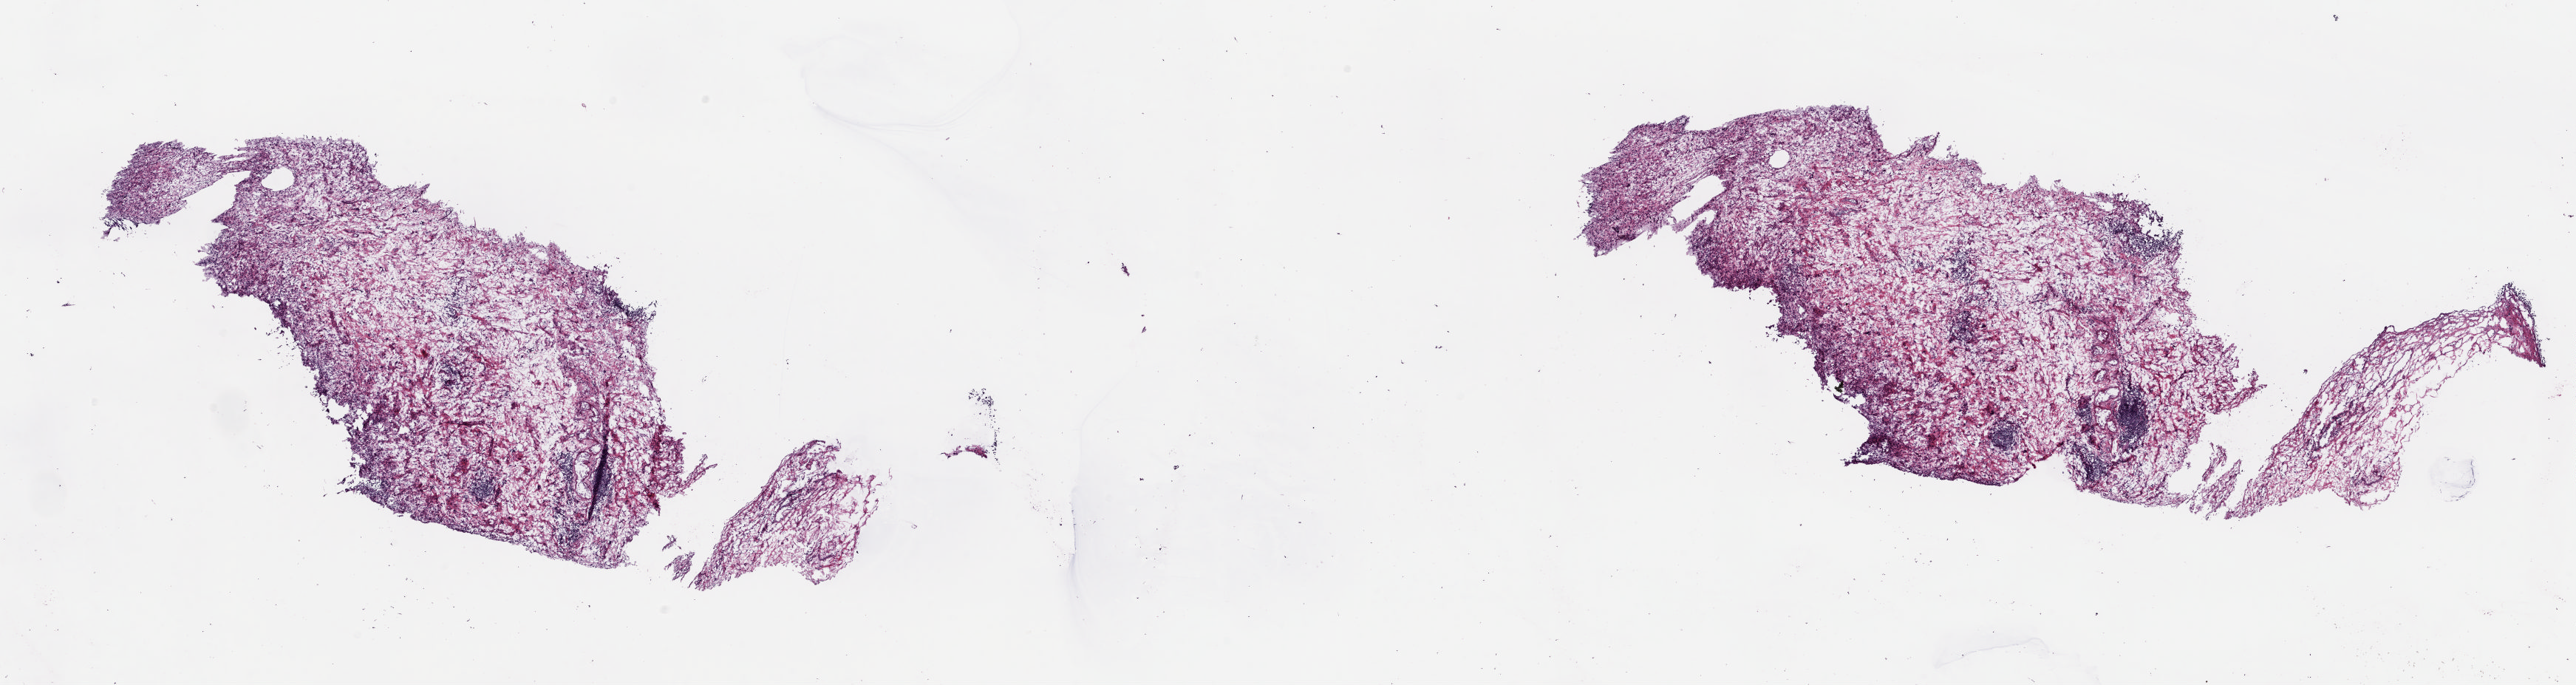
Hematoxylin and eosin (H&E) stained whole-slide image — low-resolution overview of the scanned area, about 27.7 x 7.4 mm (acquisition: 20x scan); frozen section; bladder, solid tissue normal (non-tumour tissue) sample. Male patient; age at initial diagnosis 63 years. Composition of this section per pathologist review: tumour cells 0%, tumour nuclei 0%, normal cells 0%, stromal cells 100%, necrosis 0%. Inflammatory infiltration, as recorded: lymphocyte infiltration 30%, monocyte infiltration 0%, neutrophil infiltration 5%.
This section: solid tissue normal (non-tumour) sample from the same patient. Patient diagnosis: Transitional cell carcinoma (anterior wall of bladder).